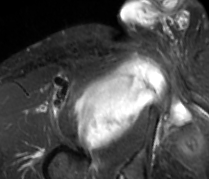
MRI of an extremity soft-tissue mass, one axial slice; position 67 of 89 along the scan axis; STIR; MR volume resampled by the dataset authors to the PET/CT grid (not the native acquisition matrix); 3.27 mm slice thickness; 209 × 179 image matrix. Male patient. Case-level facts recorded for this patient, not image findings: histological type: undifferentiated - pleiomorphic; grade: high; site of the primary tumour: right thigh.
Outlined on this slice (expert contour drawn on MRI and transferred to this co-registered scan by the dataset authors):
- gross tumour volume including surrounding oedema: bounding box [x1, y1, x2, y2] px = [75, 55, 165, 147]
- gross tumour volume (mass): [75, 59, 163, 147]